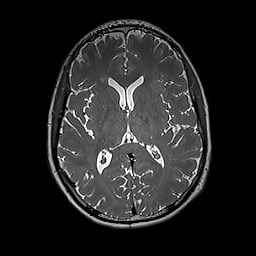
Brain MRI from a brain-tumour surgery series, one axial slice. Position 94 of 192 along the scan axis. 256 × 256 image matrix. Case-level facts recorded for this patient, not image findings: histopathology: Glioblastoma; WHO grade: 4; IDH mutation: no; tumour location: Left Insular.
Annotated regions visible in this slice (manually delineated by an expert):
- tumour: bounding box [x1, y1, x2, y2] px = [152, 76, 165, 94]